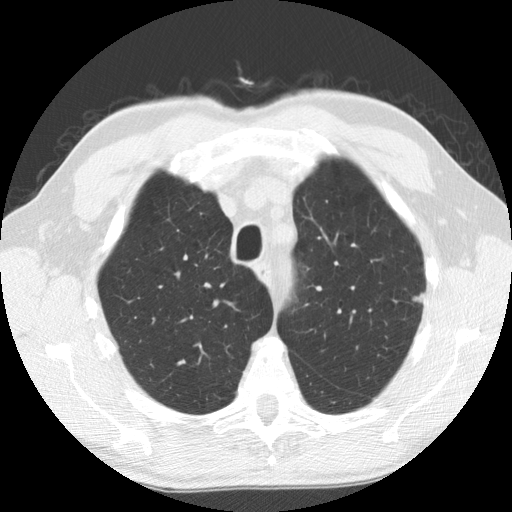
Low-dose screening chest CT, one axial slice; slice 131 of 158 in the series (ordered by position); reconstruction kernel STANDARD; 120 kVp; lung window (W 1500 / L -600 HU); 2.5 mm slice thickness; 512 × 512 image matrix, field of view 340 × 340 mm.
Annotated regions visible in this slice (outlined manually by an expert reader):
- lesion 1 (tumor, upper lobe of left lung): bounding box (x1, y1, x2, y2) in pixels: (412, 293, 424, 304)